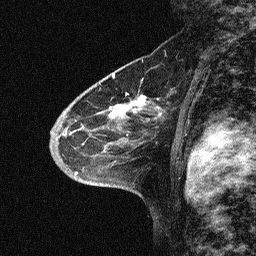
Breast MRI (dynamic contrast-enhanced), one sagittal slice. Slice 40 of 64 in the series (ordered by position). Dynamic contrast-enhanced study with each time point stored as its own series, time point 2 of 3 at this slice position (early post-contrast, ordered by acquisition time). 1.5 T. TE 4.5 ms, TR 11 ms. 2.06 mm slice thickness. 256 × 256 image matrix. Female patient, age 46 years. Case-level facts recorded for this patient, not image findings: setting: breast cancer imaged before/during neoadjuvant chemotherapy; receptor status: HER2-positive.
Annotated regions visible in this slice (semi-automatic segmentation, software-assisted and operator-edited):
- analysis volume of interest (the breast-tissue region the enhancement analysis was run in; not a lesion): box from (x=46, y=51) to (x=180, y=169) px
- tumour enhancement mask (voxels above the 90 % enhancement threshold inside the analysis volume of interest): (x=108, y=95)–(x=144, y=118)